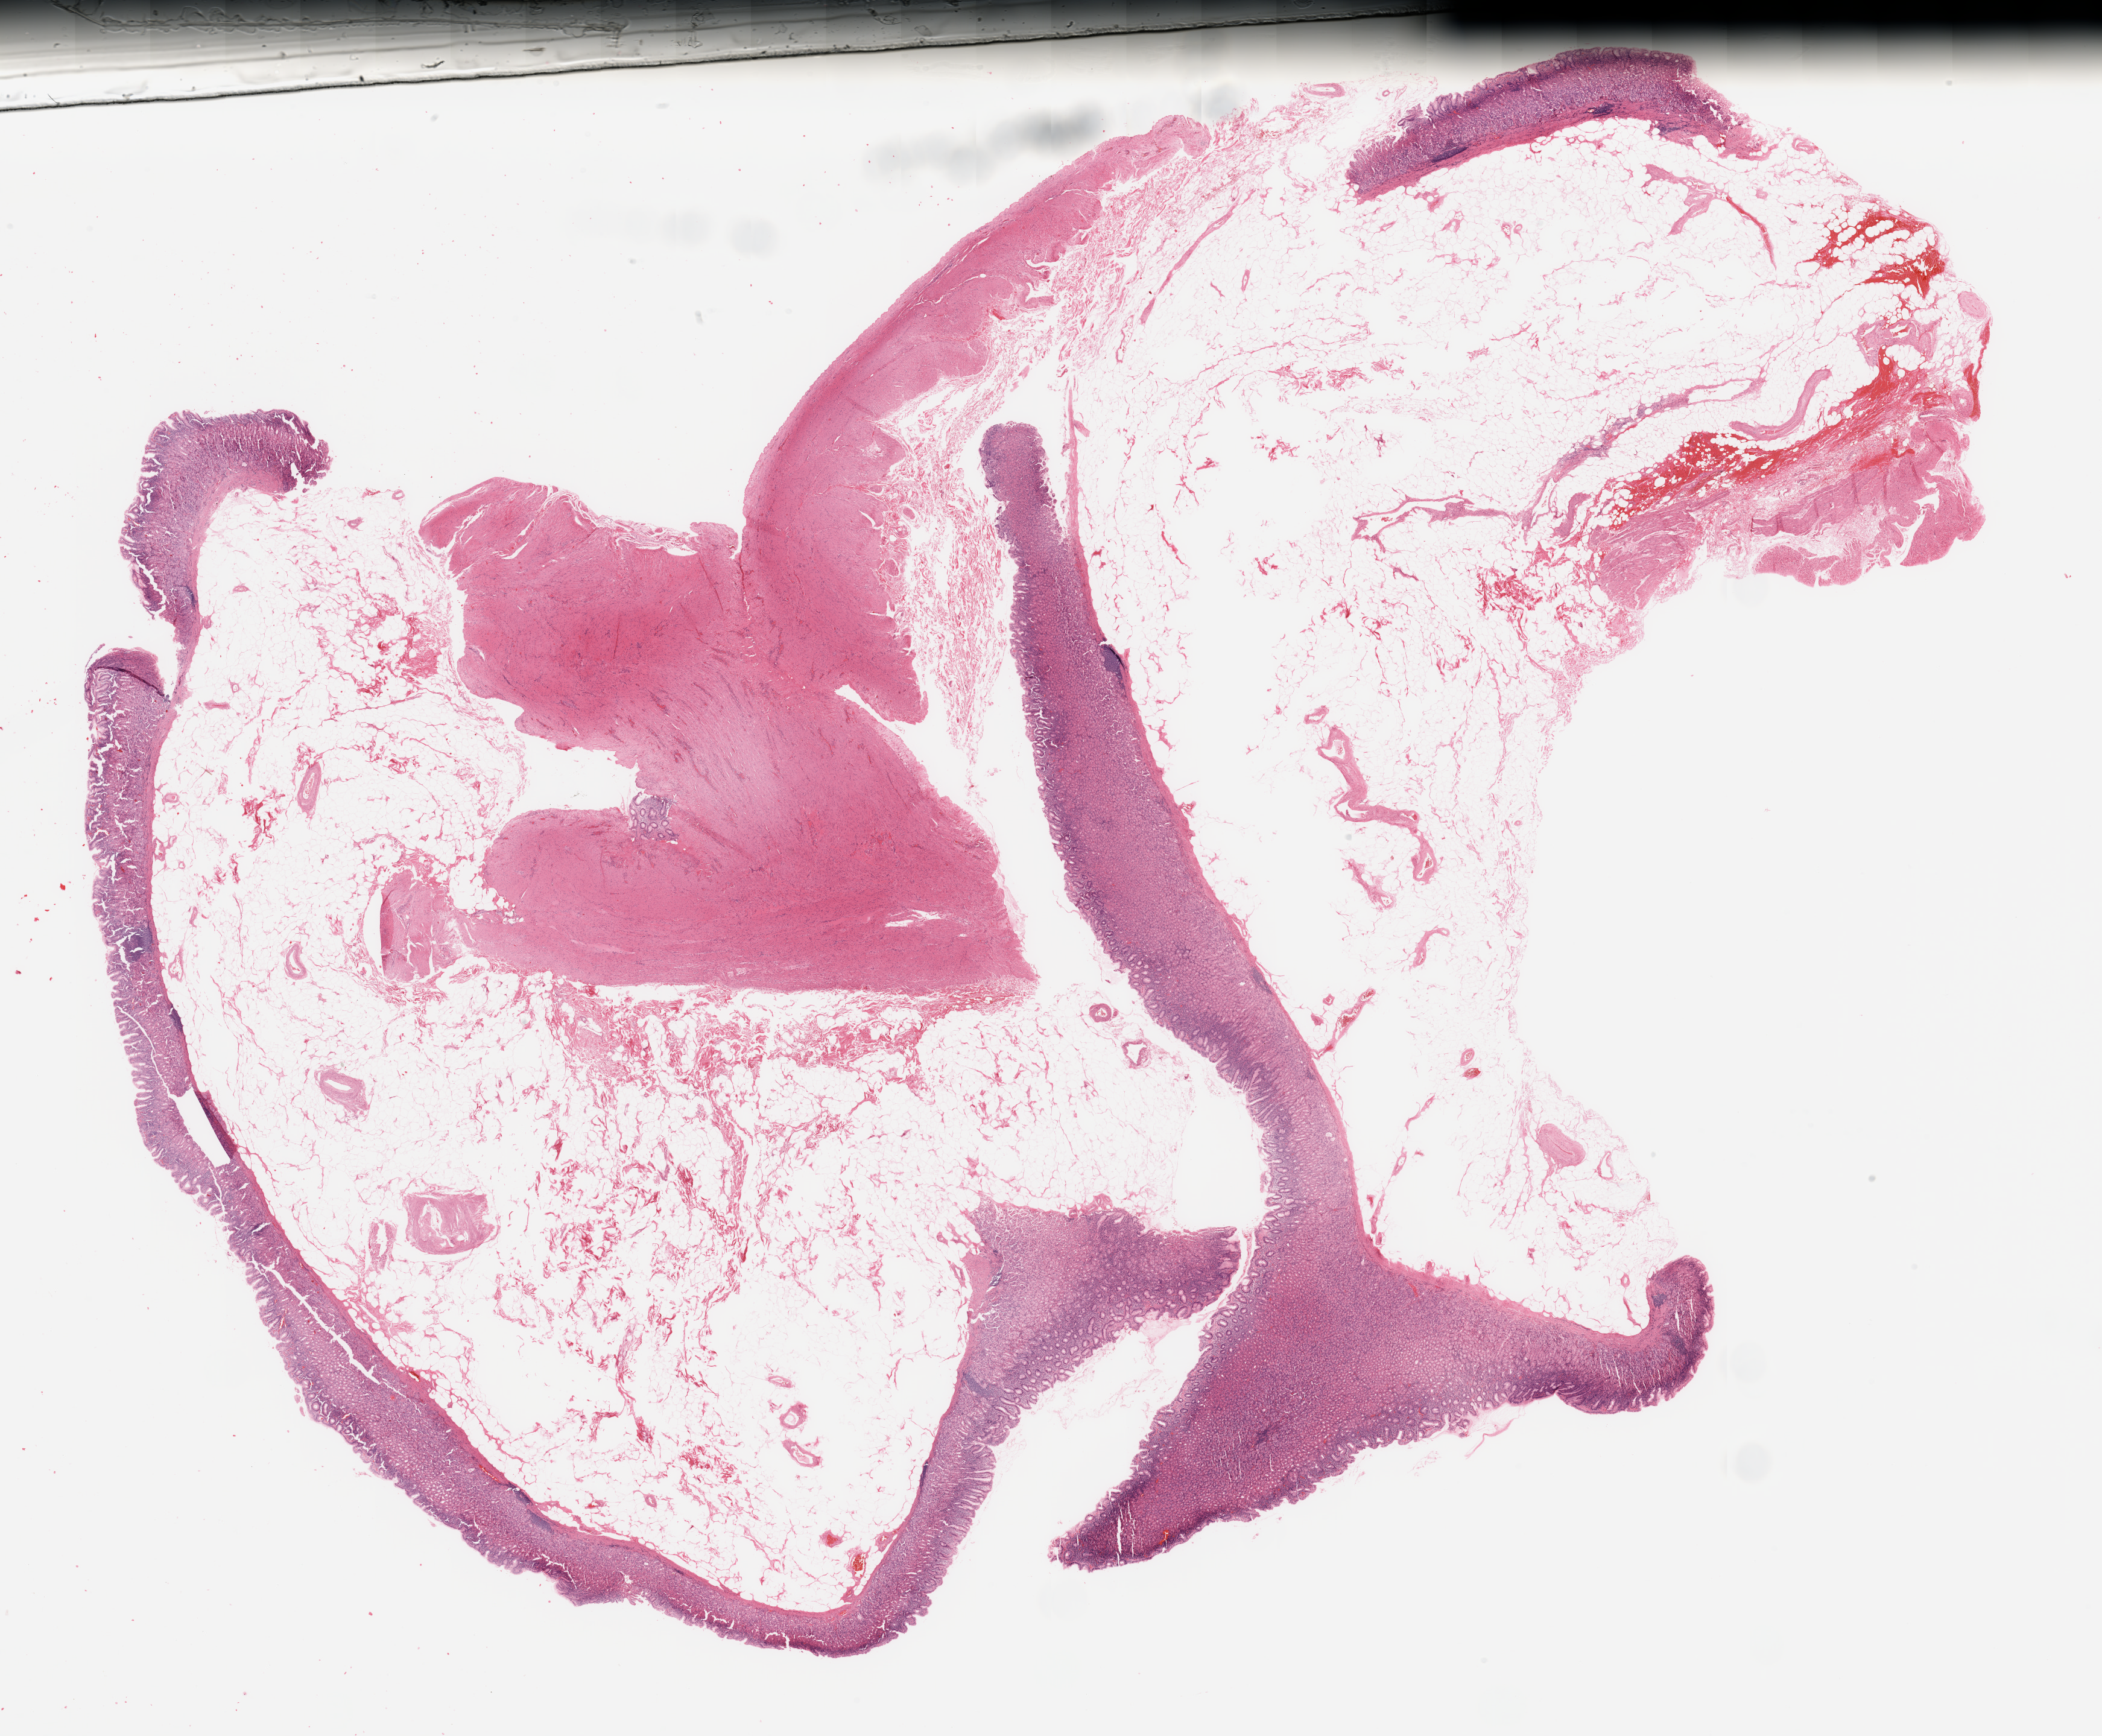
H&E whole-slide image, whole scanned area (about 27.6 x 22.8 mm, slide scanned at 20x) shown as a low-resolution overview. Female, 73 y/o.
• patient diagnosis (cohort enrolment): sarcoma (site not recorded at cohort level)